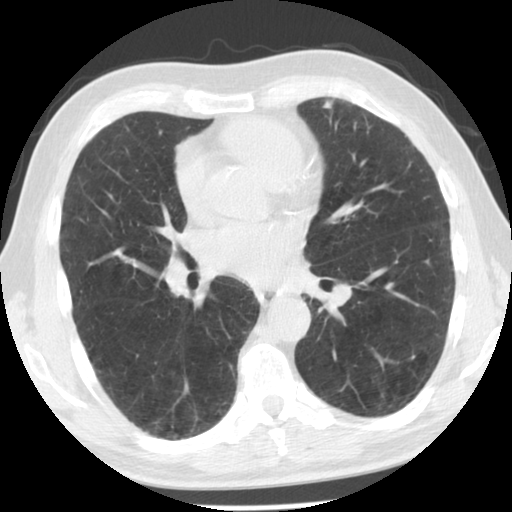
Low-dose screening chest CT, axial slice, second screening round (one year after baseline), lung window (W 1500 / L -600 HU), 2.5 mm slice thickness, slice 64 of 129 in the series, 512 × 512 image matrix. Male, age 66 years at enrolment. Former smoker at enrolment.
Expert-annotated lung lesion, bounding box (x1, y1, x2, y2) in pixels: (307, 89, 346, 126). The exam's reader record, not a measurement of the box and not confirmed to be the same lesion: non-calcified nodule or mass ≥4 mm, lingula, 6 × 5 mm, smooth margins, soft tissue attenuation, pre-existing on the prior screen: yes; interval growth: yes. Participant outcome: lung cancer diagnosed 148 days after this screen — adenocarcinoma, NOS, left upper lobe, moderately differentiated (G2), stage IIB (AJCC 6th edition), 9 mm at pathology.